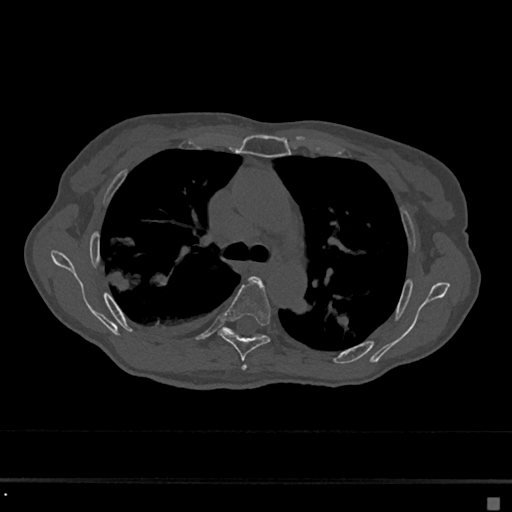
CT including the spine, one axial slice; slice 457 of 797 in the series (ordered by position); bone window (W 1800 / L 400 HU); 0.5 mm slice thickness; 512 × 512 image matrix. Female patient, age 68 years. From the clinical record (not read from this slice): primary cancer: renal.
Annotated regions visible in this slice (semi-automatic segmentation, software-assisted and operator-edited):
- T4 vertebra: bounding box <242,282,262,371> (left, top, right, bottom; pixels)
- T5 vertebra: <219,278,271,361>
- T6 vertebra: <224,328,264,338>